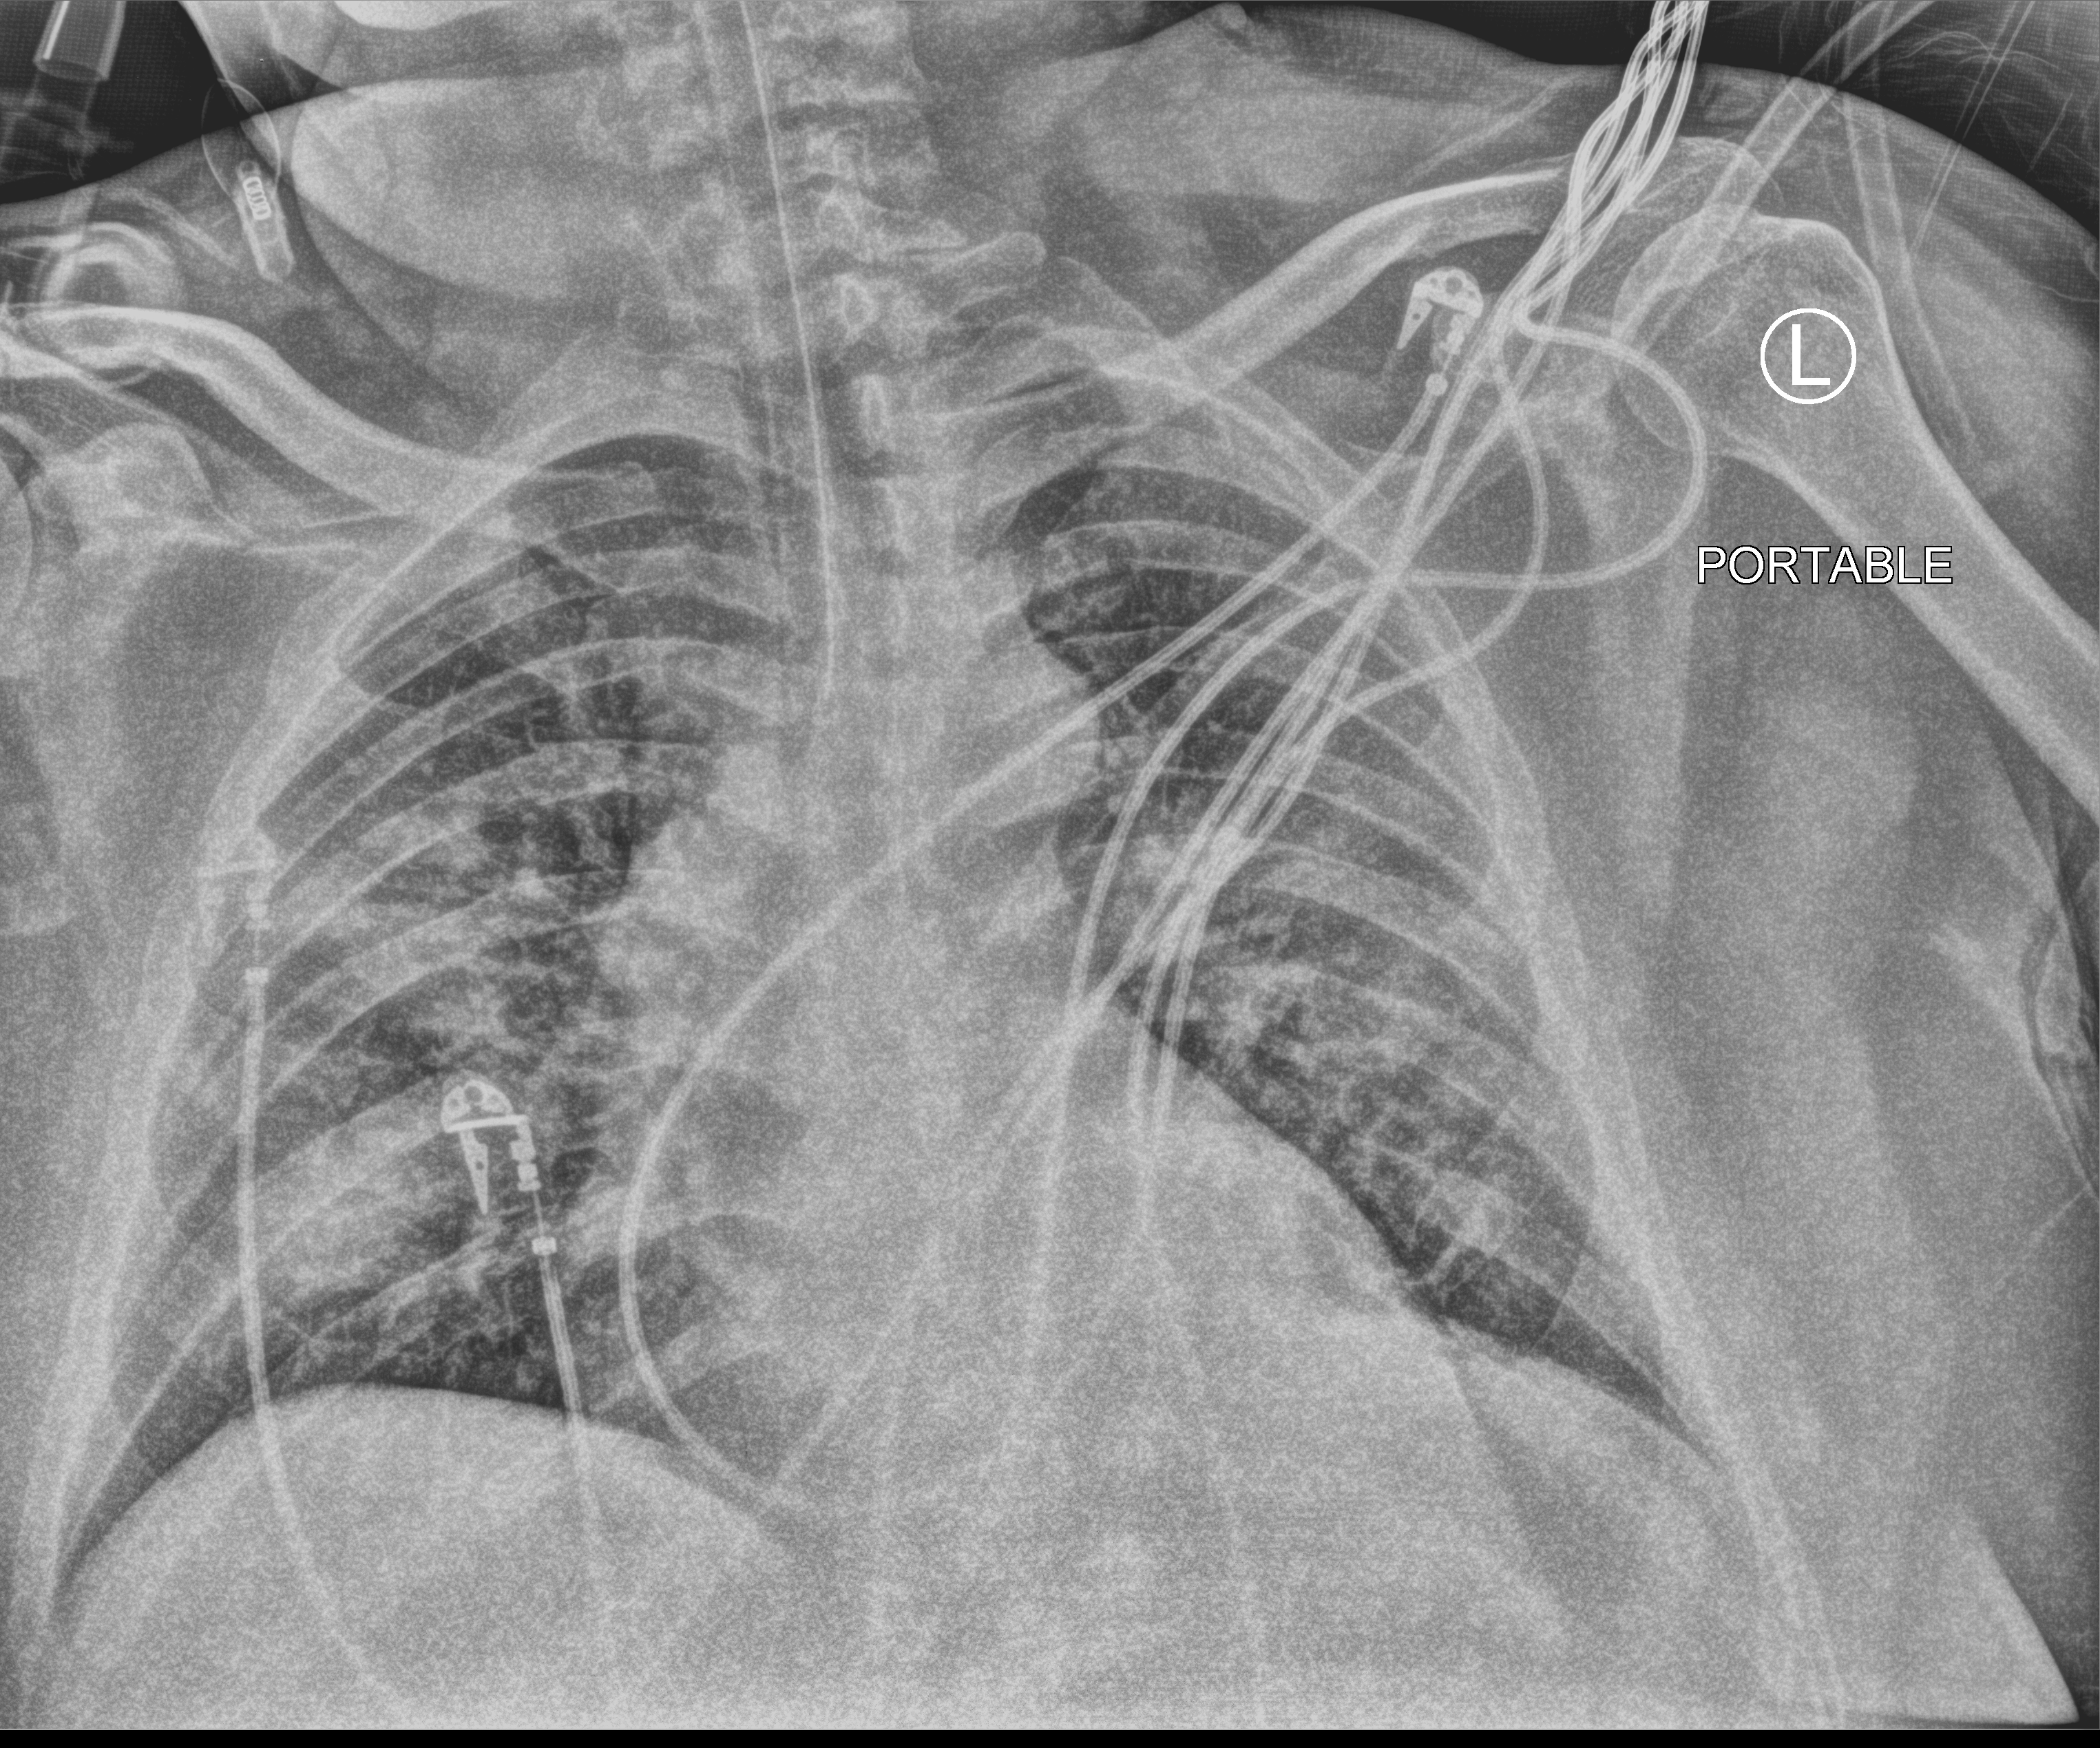
Bedside chest radiograph (computed radiography), anteroposterior (AP) projection. Patient hospitalised with COVID-19; male, aged 60–74 years.
Admission-level facts for this patient (not findings on this image; timing relative to this image not recorded):
- admitted to intensive care during this hospital stay: yes